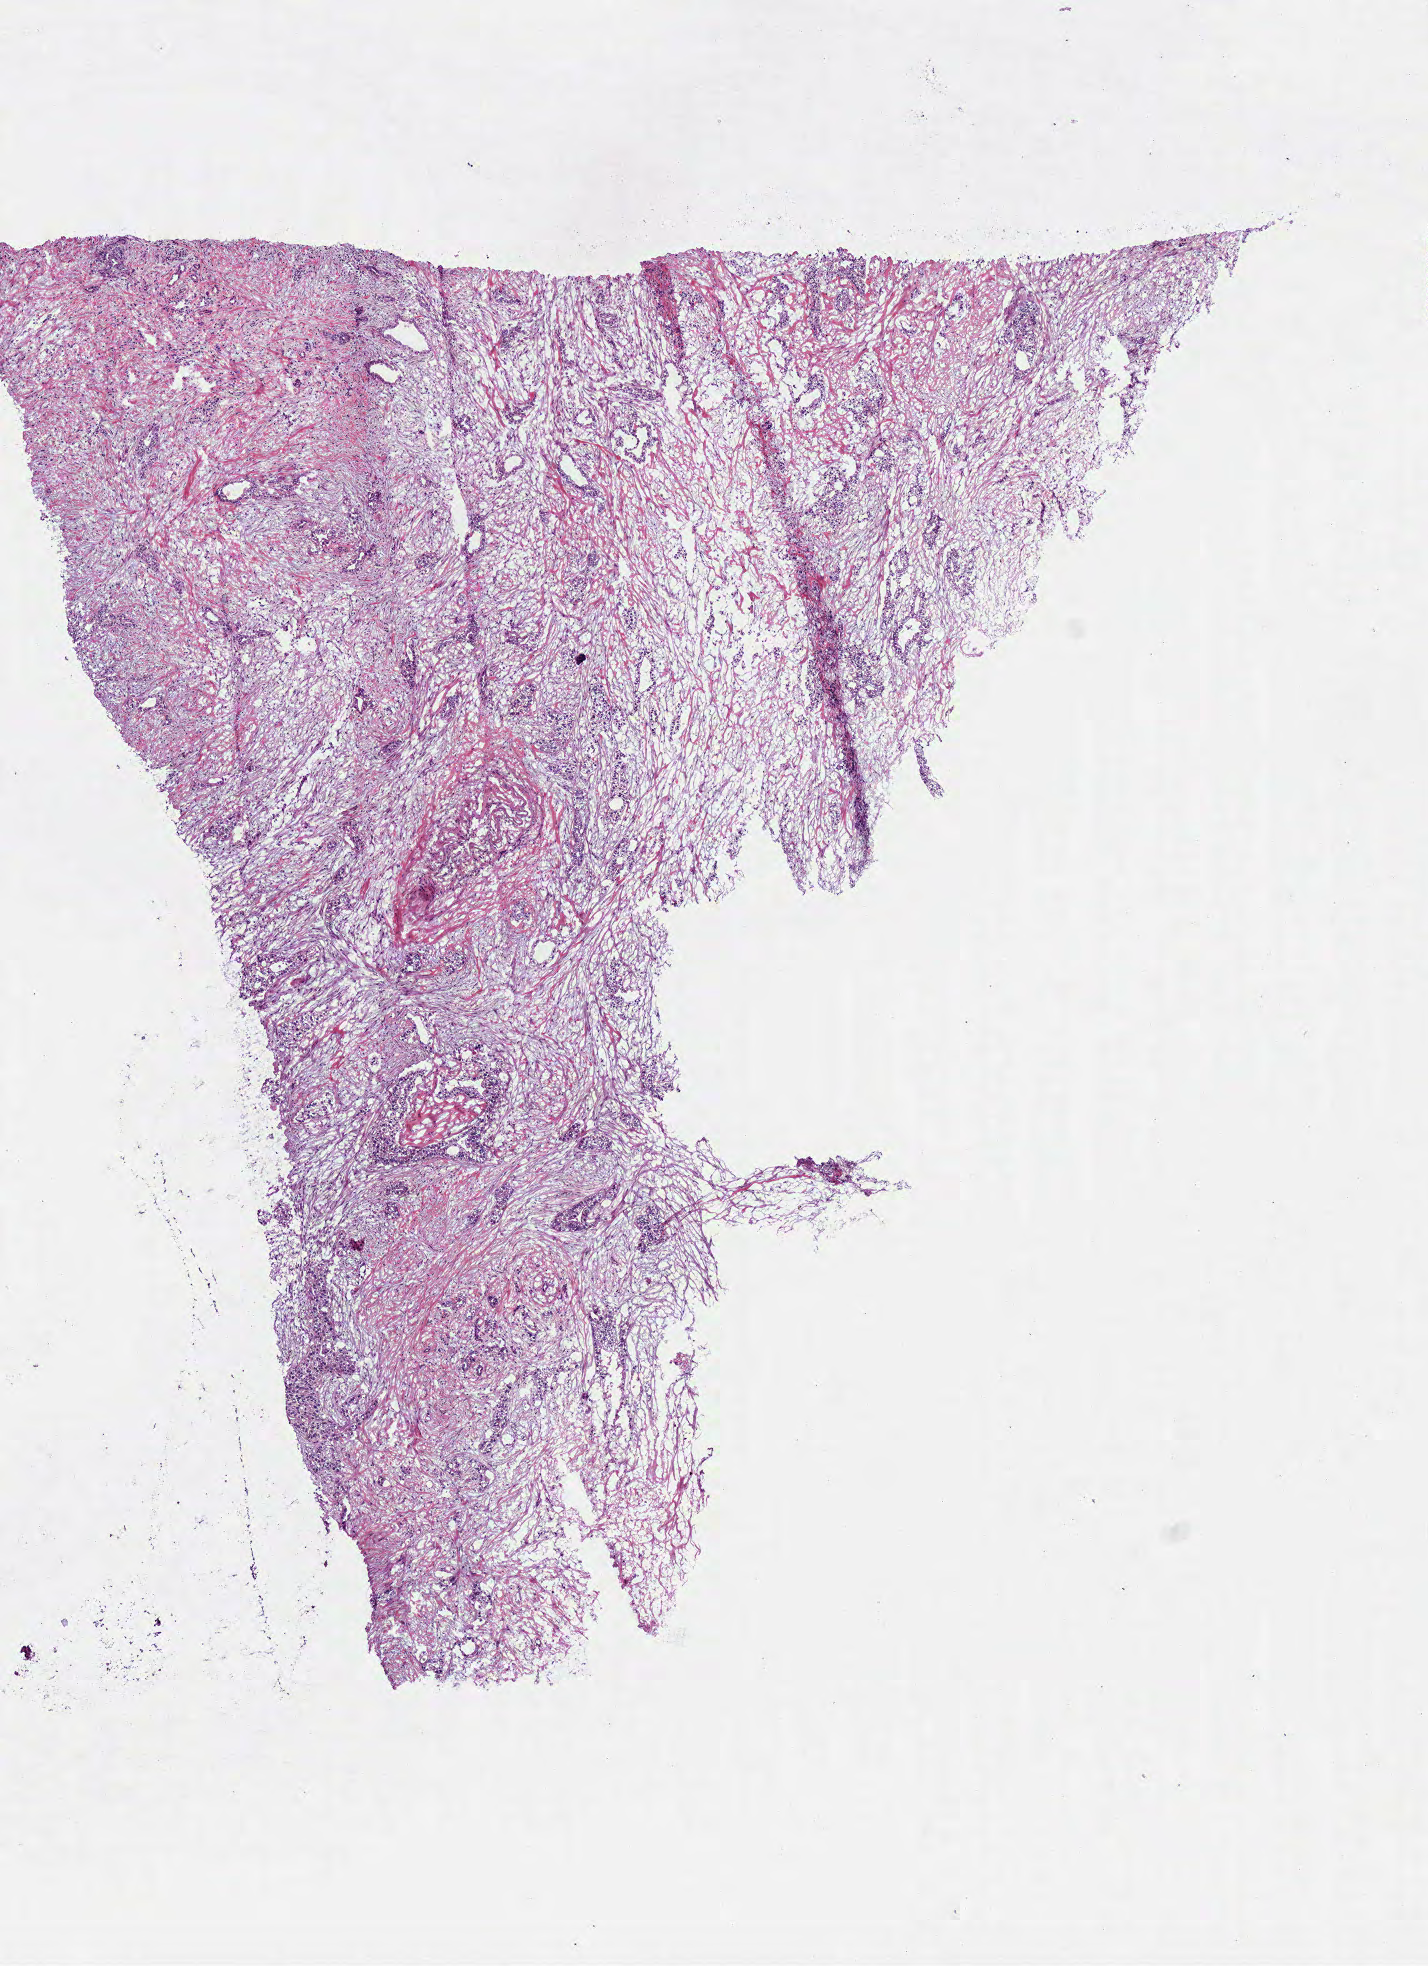
Digitized H&E tissue section (whole slide), a low-resolution overview of the entire scanned area, about 5.6 x 7.7 mm, frozen section from the top of the tissue portion, primary tumour sample from the pancreas. Male, age 83 years at initial diagnosis. Histologic grade: G3 (poorly differentiated). Composition of this section per pathologist review: tumour cells 60%, tumour nuclei 75%, normal cells 0%, stromal cells 40%, necrosis 0%.
• pathologic diagnosis: Infiltrating duct carcinoma, NOS (head of pancreas)
• AJCC pathologic stage: IIA (6th edition)
• lymph nodes positive (case pathology): 2 of 18 examined